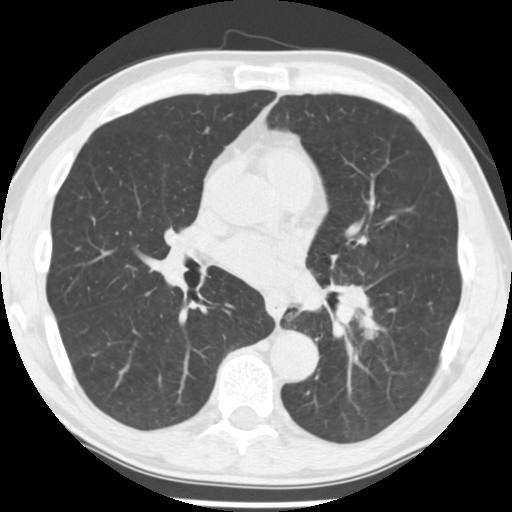
Chest CT (low-dose screening protocol), one axial image. Third annual screen. Lung window (W 1500 / L -600 HU). Slice 120 of 242 in the series. Male, age 64 years at enrolment.
Lesion marked by an expert reader, box from (x=349, y=315) to (x=390, y=352) px. No non-calcified nodule or mass ≥4 mm was recorded by the screening reader at this exam. Participant outcome: lung cancer diagnosed 203 days after this screen — adenocarcinoma, NOS, left lower lobe, stage IV (AJCC 6th edition), 44 mm at pathology.